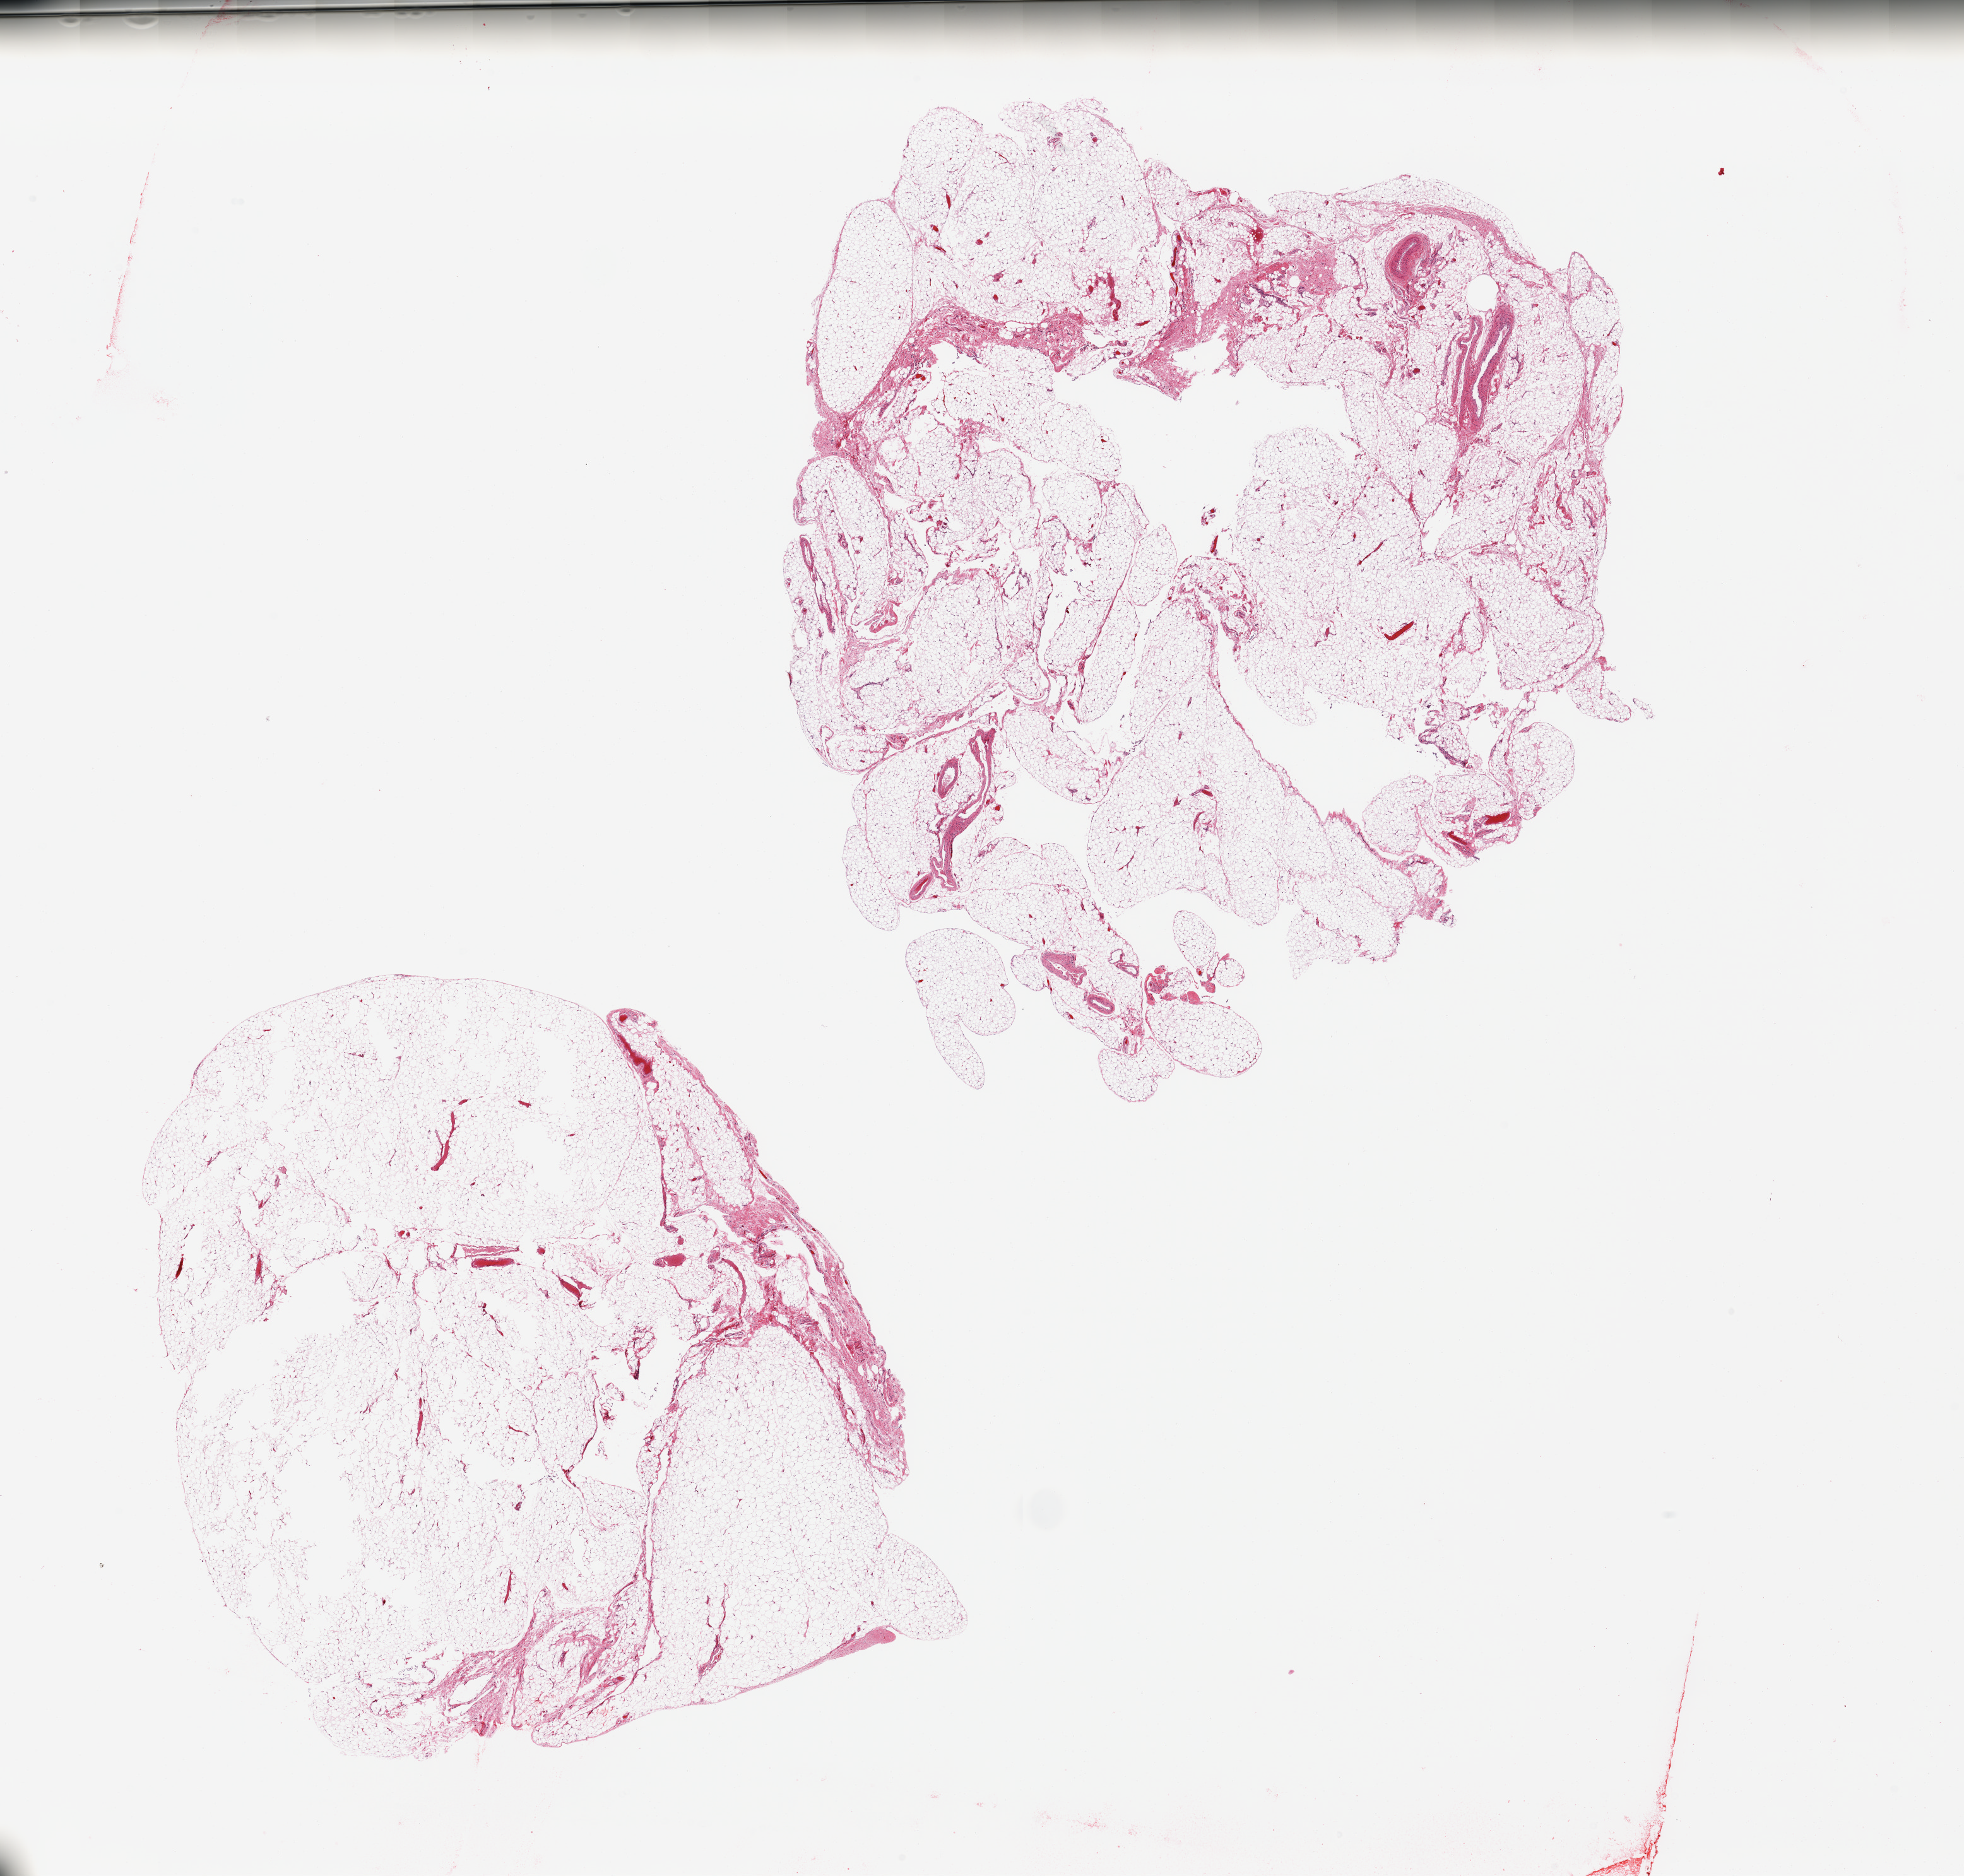
Whole-slide image, H&E stain — whole scanned area (about 24.6 x 23.5 mm) shown as a low-resolution overview. PAXgene-fixed paraffin-embedded (PFPE) section. Section of omentum (target tissue). Tissue donor sample. Female donor.
- pathologist's review note for this sample: 2 pieces, fascia/mesothelial hyperplasia, vascular elements are ~10% of tissue